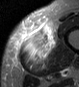
MRI of an extremity soft-tissue mass, one axial slice; position 12 of 45 along the scan axis; STIR; MR volume resampled by the dataset authors to the PET/CT grid (not the native acquisition matrix); 3.27 mm slice thickness; 79 × 87 image matrix, field of view 77 × 85 mm. Male patient. Case-level facts recorded for this patient, not image findings: histological type: pleiomorphic leiomyosarcoma; grade: high; site of the primary tumour: left thigh.
Annotated regions visible in this slice (expert contour drawn on MRI and transferred to this co-registered scan by the dataset authors):
- gross tumour volume including surrounding oedema: bounding box <20,20,57,70> (left, top, right, bottom; pixels)
- gross tumour volume (mass): <24,25,53,56>